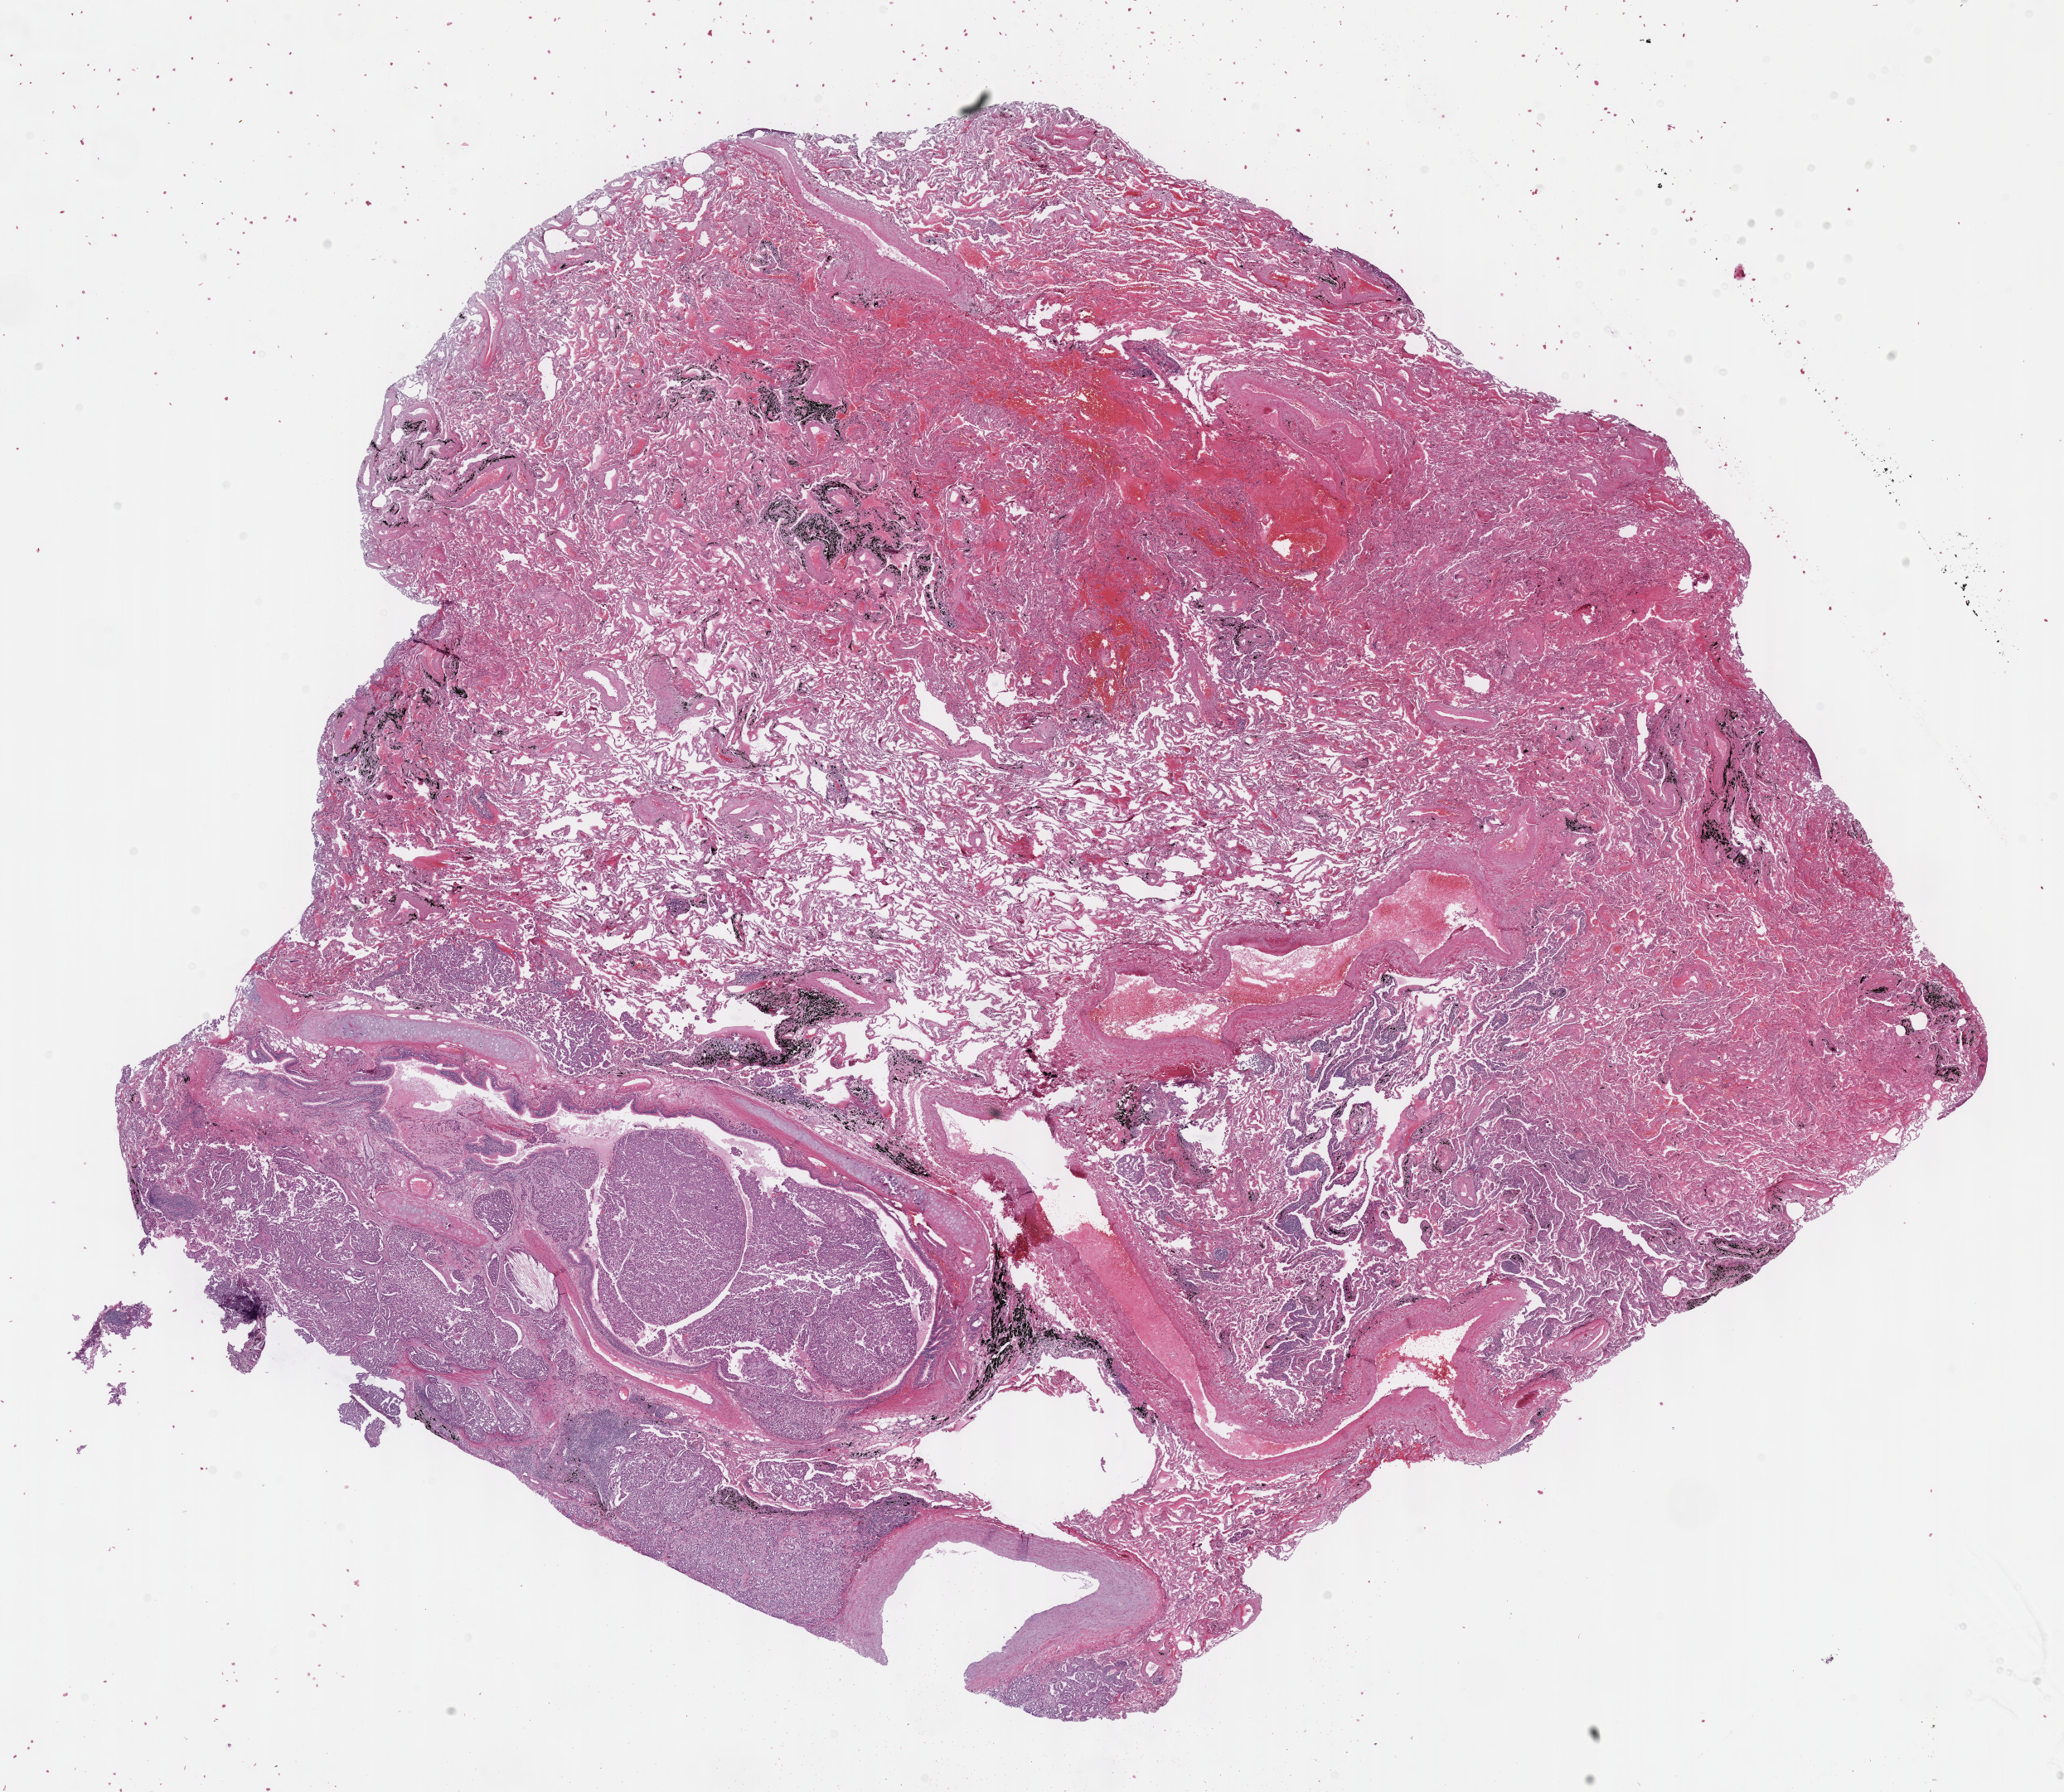
Digitized H&E tissue section (whole slide), whole scanned area (about 20.1 x 17.5 mm) shown as a low-resolution overview; formalin-fixed paraffin-embedded (FFPE) diagnostic section; lung, primary tumour sample. Male, age 71 years at initial diagnosis.
• AJCC pathologic stage: IA (6th edition)
• TNM: T1 N0 M0
• pathologic diagnosis: Adenocarcinoma, NOS (lower lobe, lung)